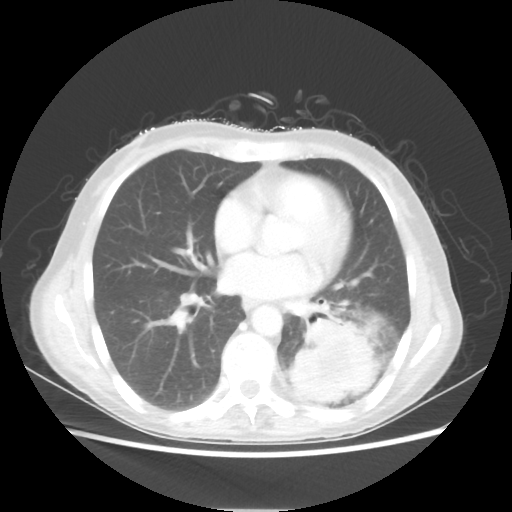
Chest CT, one axial slice. Position 26 of 56 along the scan axis. 80 kVp. Lung window (W 1500 / L -600 HU). 5 mm slice thickness. 512 × 512 image matrix. Female patient, age 53 years. From the clinical record (not read from this slice): clinical TNM (as recorded): T3 N0 M0.
Structures marked on this image (bounding box drawn by a radiologist):
- lung tumour (recorded histology: adenocarcinoma): bounding box (x1, y1, x2, y2) in pixels: (287, 318, 379, 403)